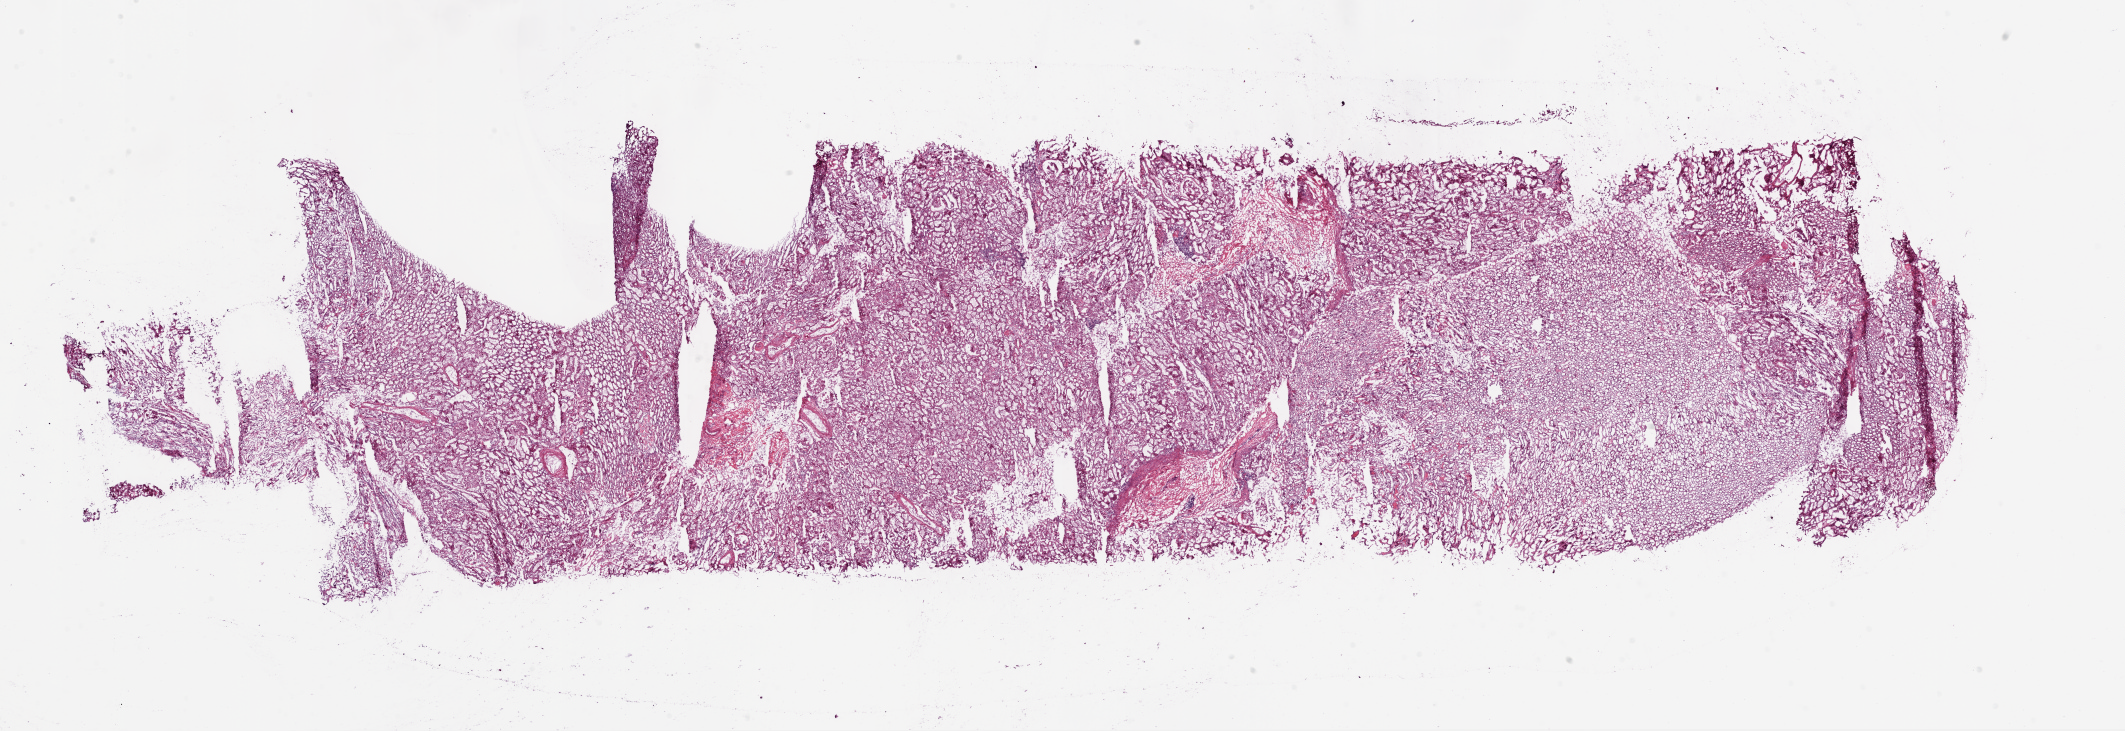
Hematoxylin and eosin (H&E) stained whole-slide image, shown as a low-resolution overview of the whole scanned area (about 34.1 x 11.7 mm, slide scanned at 20x). Frozen section from the bottom of the tissue portion. Solid tissue normal (non-tumour tissue) sample from the kidney. Female, age 49 years at initial diagnosis.
This section: solid tissue normal sample (biorepository sample class). Patient diagnosis: Clear cell adenocarcinoma, NOS.